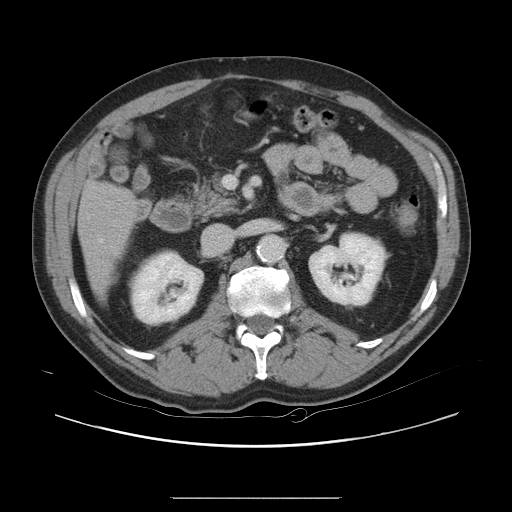
Contrast-enhanced abdominal CT, one axial slice. Position 8 of 40 along the scan axis. 120 kVp. Intravenous contrast given. Soft-tissue window (W 400 / L 40 HU). 5 mm slice thickness. 512 × 512 image matrix, field of view 408 × 408 mm. Male patient, age 64 years. Case-level facts recorded for this patient, not image findings: diagnosis: colorectal cancer liver metastases, imaged before liver resection; multiple liver metastases: yes; largest metastasis: 3.2 cm; disease in both lobes: yes.
Structures marked on this image (outlined manually by an expert reader):
- hepatic veins: bounding box <99,240,103,243> (left, top, right, bottom; pixels)
- liver: <79,182,136,289>